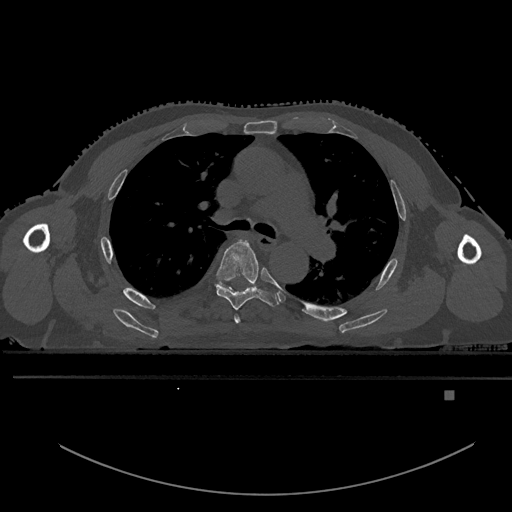
CT including the spine, one axial slice. Slice 358 of 969 in the series (ordered by position). Bone window (W 1800 / L 400 HU). 512 × 512 image matrix, field of view 456 × 456 mm. Male patient, age 82 years. From the clinical record (not read from this slice): primary cancer: prostate; vertebrae with lytic lesions (as recorded): T11, T9, T8, T2.
Outlined on this slice (semi-automatically segmented with operator editing):
- T4 vertebra: bounding box <234,315,241,324> (left, top, right, bottom; pixels)
- T5 vertebra: <216,240,279,311>